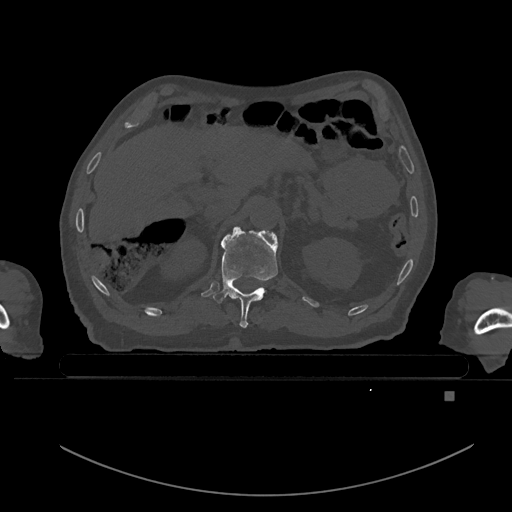
CT including the spine, one axial slice; slice 18 of 969 in the series (ordered by position); bone window (W 1800 / L 400 HU); 0.5 mm slice thickness; 512 × 512 image matrix, field of view 456 × 456 mm. Patient: male, 82 years. From the clinical record (not read from this slice): primary cancer: prostate; vertebrae with lytic lesions (as recorded): T11, T9, T8, T2.
Outlined on this slice (semi-automatically segmented with operator editing):
- T11 vertebra: bounding box [x1, y1, x2, y2] px = [213, 228, 278, 328]